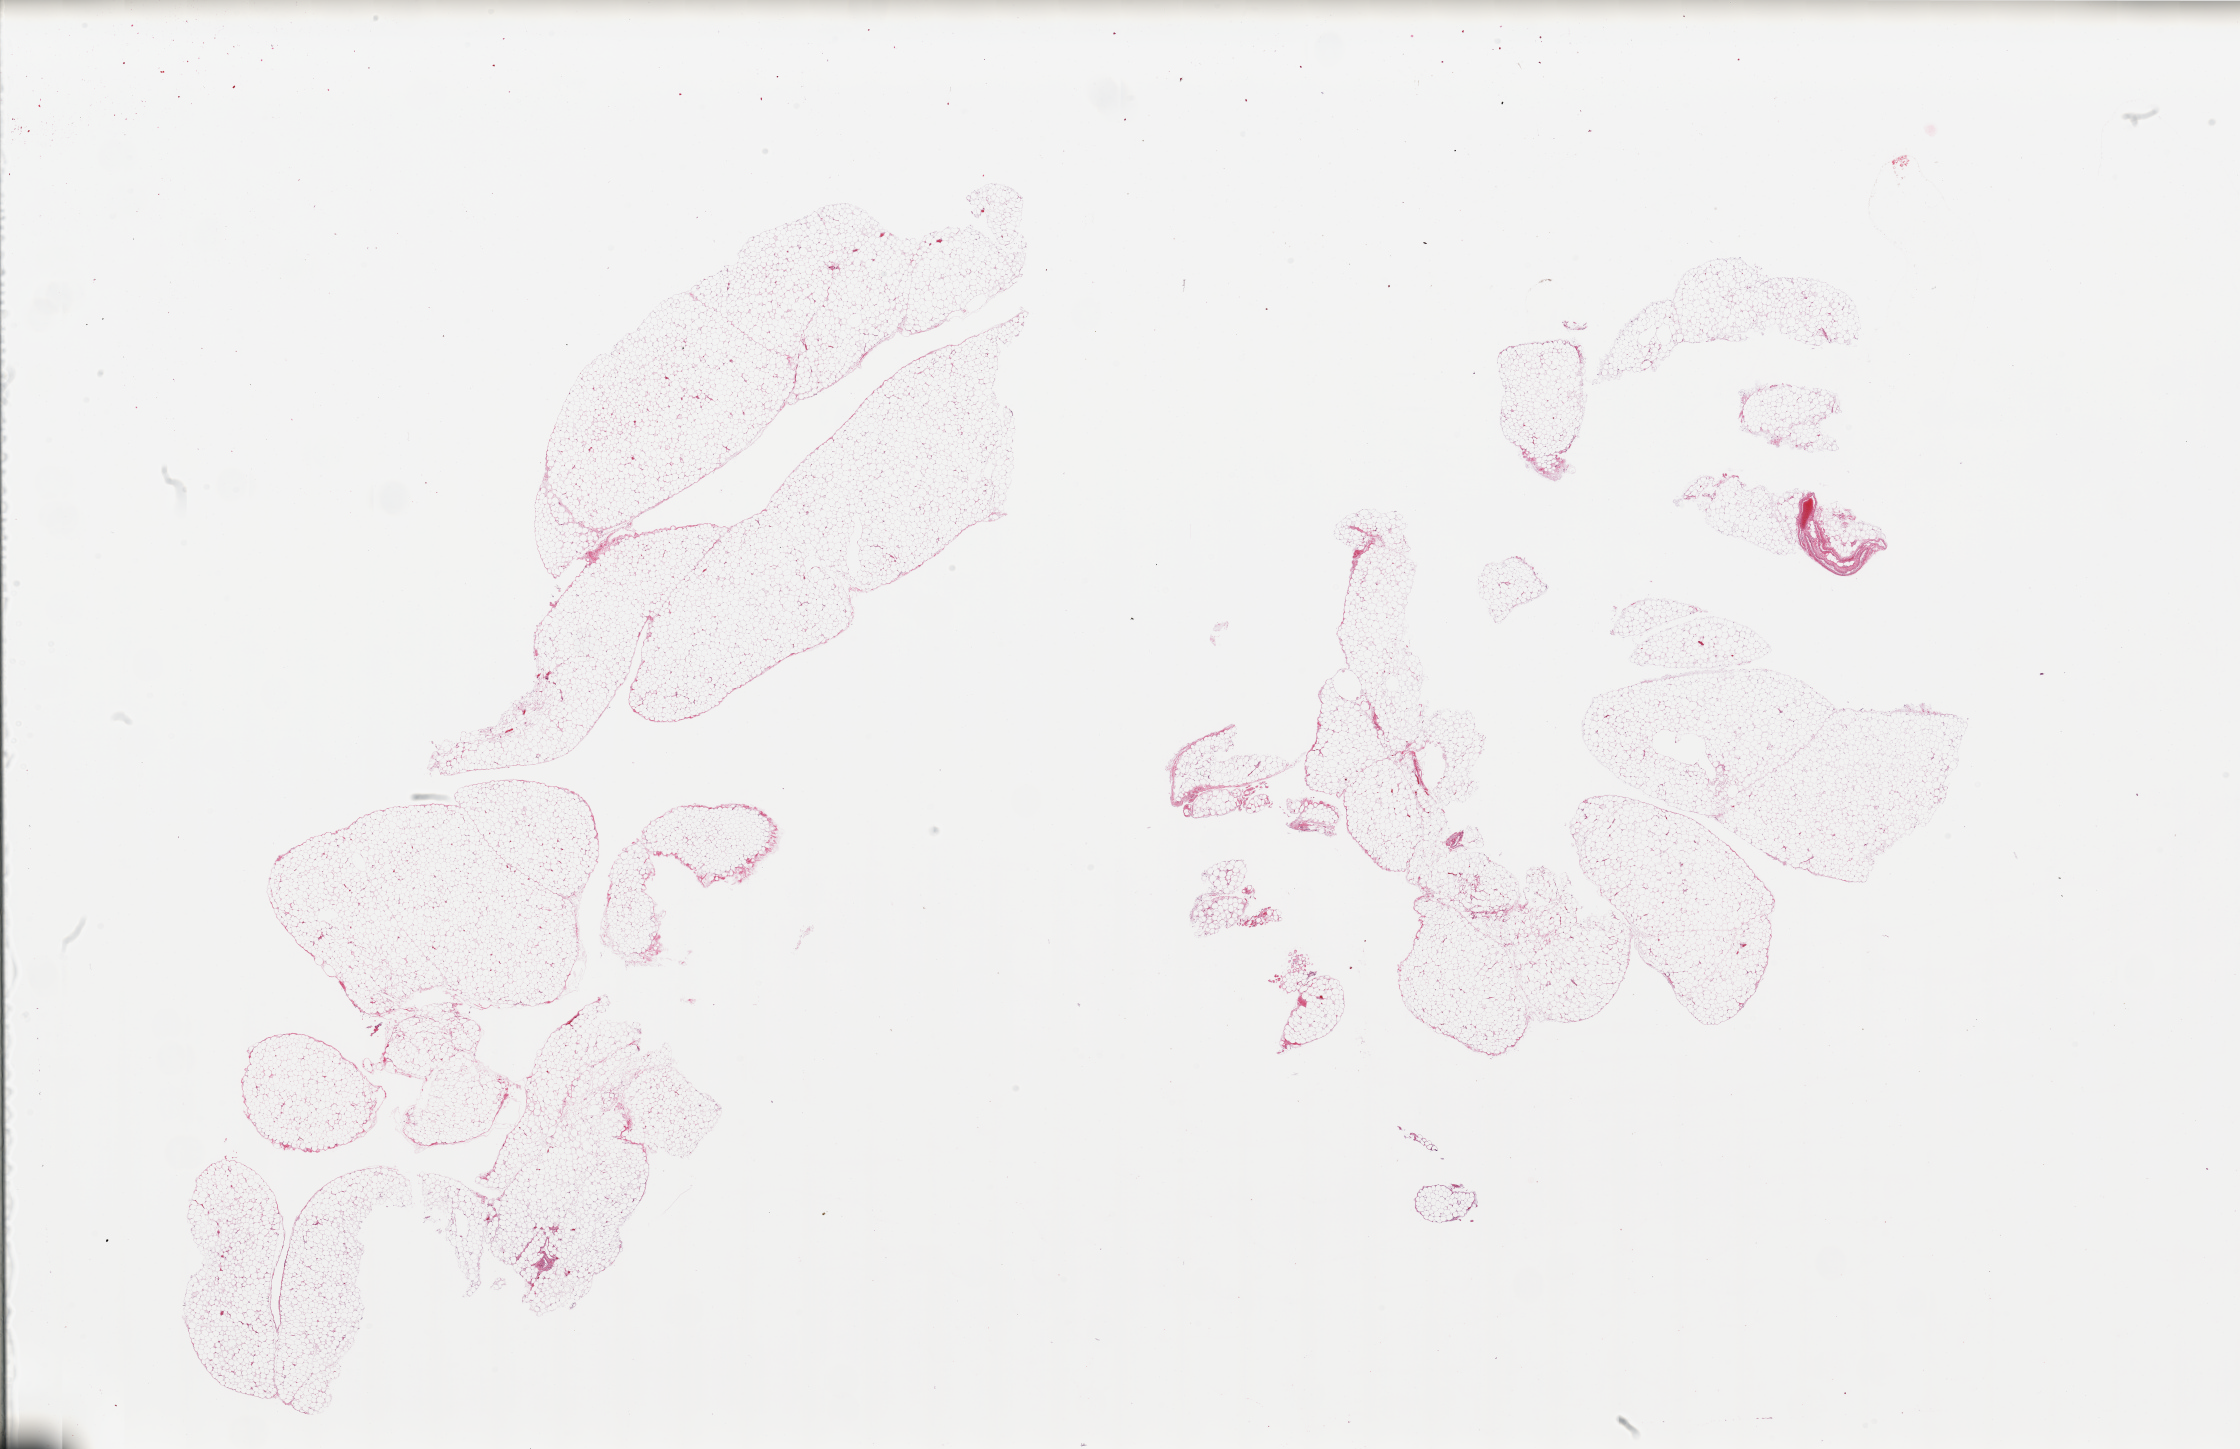
Digitized haematoxylin and eosin-stained section — whole scanned area (about 35.4 x 22.9 mm, slide scanned at 20x) shown as a low-resolution overview, PAXgene-fixed paraffin-embedded (PFPE) section, target tissue: omentum, tissue donor sample. Male donor.
Pathologist's review note for this sample: 2 pieces, trace vascular elements.